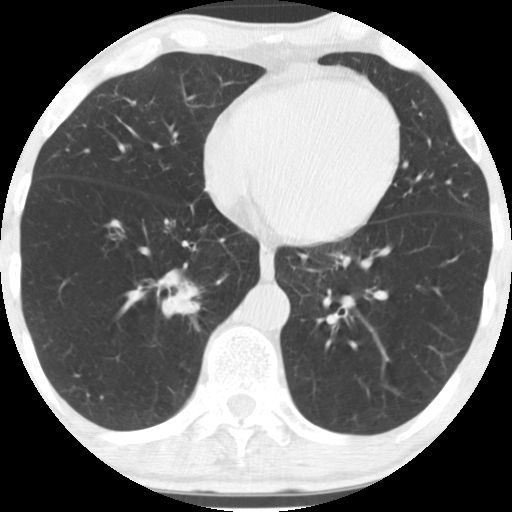
Low-dose screening chest CT, one axial slice; slice 56 of 170 in the series (ordered by position); reconstruction kernel STANDARD; lung window (W 1500 / L -600 HU); 512 × 512 image matrix, field of view 290 × 290 mm.
Outlined on this slice (outlined manually by an expert reader):
- lesion 1 (tumor, lower lobe of right lung): box from (x=171, y=286) to (x=198, y=314) px